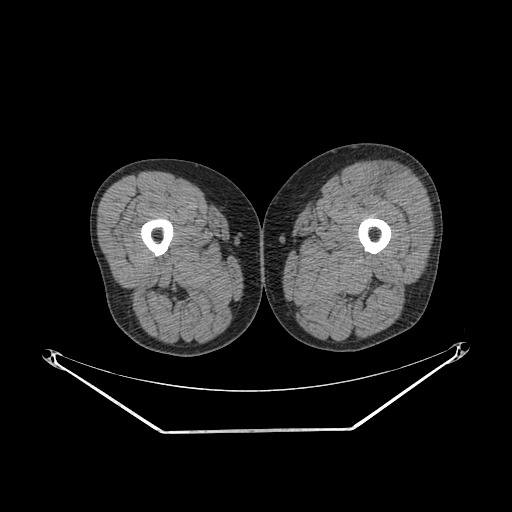
CT of an extremity soft-tissue mass (from a PET/CT study), one axial slice. Position 220 of 267 along the scan axis. Soft-tissue window (W 400 / L 40 HU). 3.75 mm slice thickness. 512 × 512 image matrix, field of view 500 × 500 mm. Male patient. From the clinical record (not read from this slice): histological type: extraskeletal osteosarcoma; grade: high; site of the primary tumour: thigh.
Outlined on this slice (expert contour drawn on MRI and transferred to this co-registered scan by the dataset authors):
- gross tumour volume (mass): bounding box (x1, y1, x2, y2) in pixels: (379, 174, 401, 202)